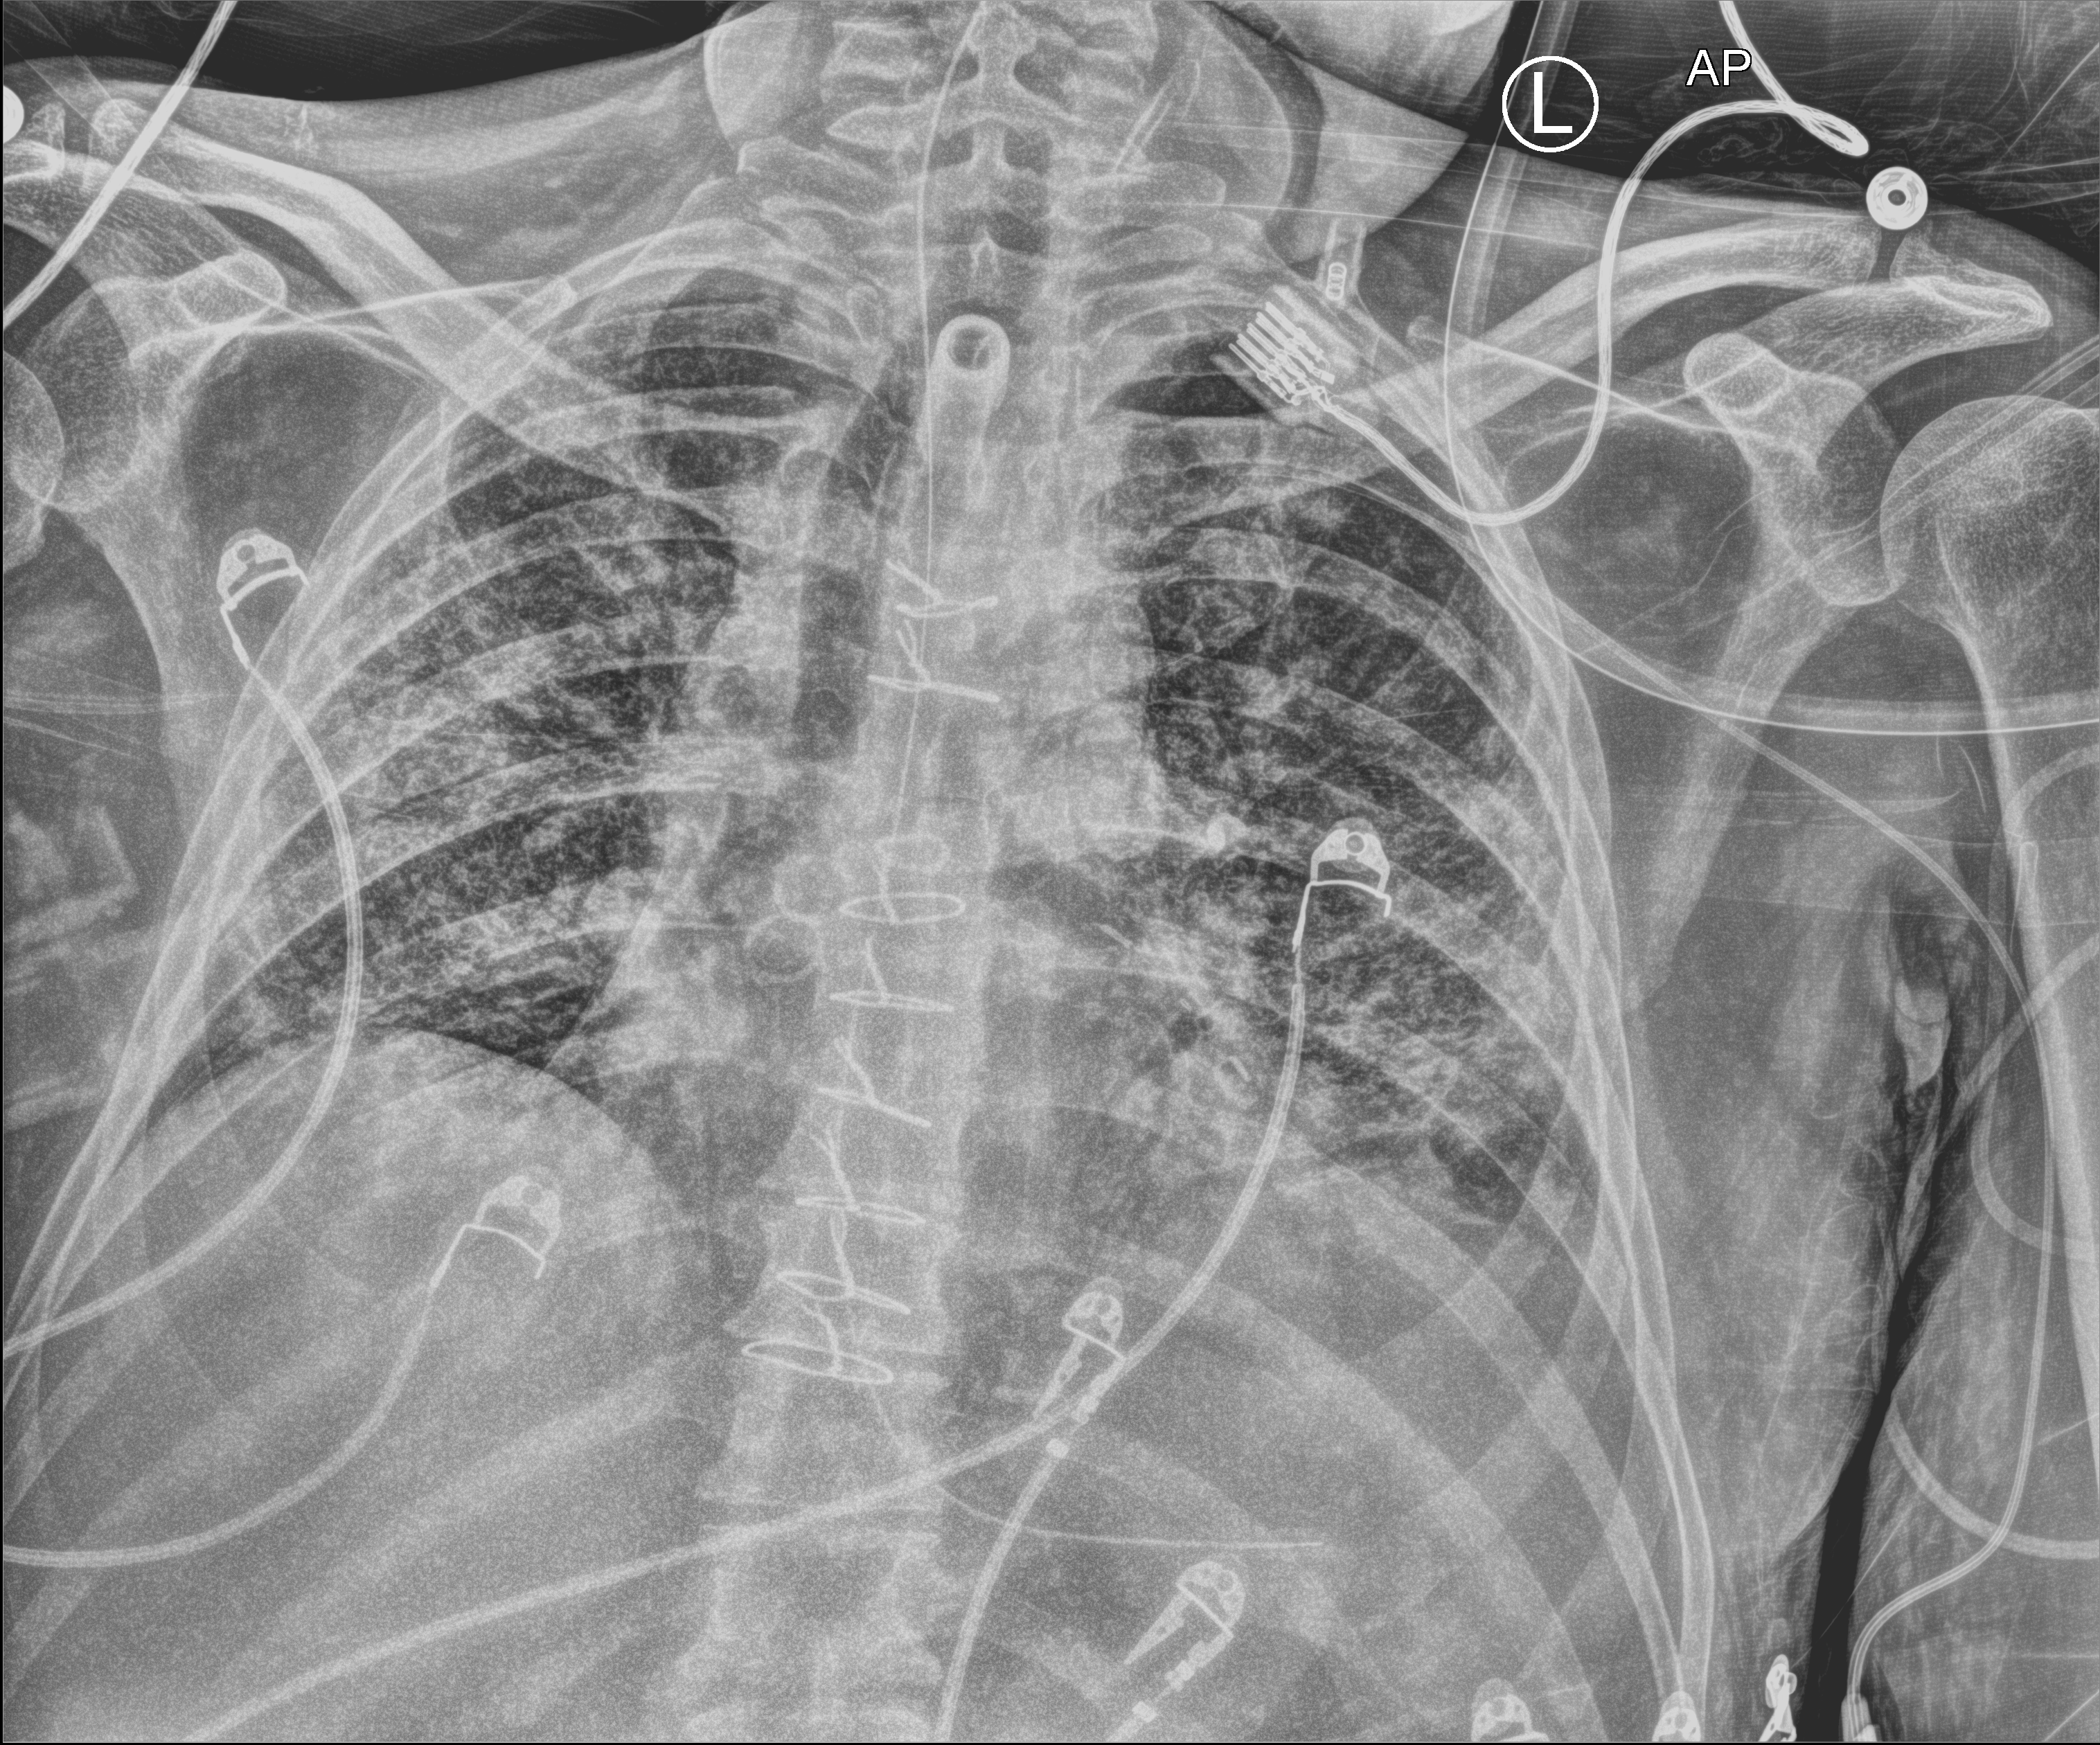
Chest X-ray (portable), anteroposterior (AP) projection. Patient hospitalised with COVID-19; male, aged 18–59 years.
Admission-level facts for this patient (not findings on this image; timing relative to this image not recorded):
- mechanically ventilated during this hospital stay: yes
- smoking status (admission record): former